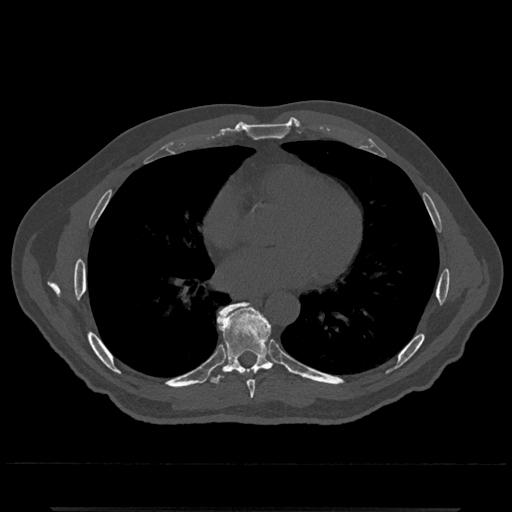
CT including the spine, one axial slice; position 688 of 797 along the scan axis; reconstruction kernel Br40s/3; 120 kVp; bone window (W 1800 / L 400 HU); 512 × 512 image matrix, field of view 393 × 393 mm. Male patient, age 67 years. Case-level facts recorded for this patient, not image findings: primary cancer: prostate.
Structures marked on this image (semi-automatically segmented with operator editing):
- T7 vertebra: bounding box [x1, y1, x2, y2] px = [247, 368, 262, 399]
- T8 vertebra: [208, 302, 275, 385]